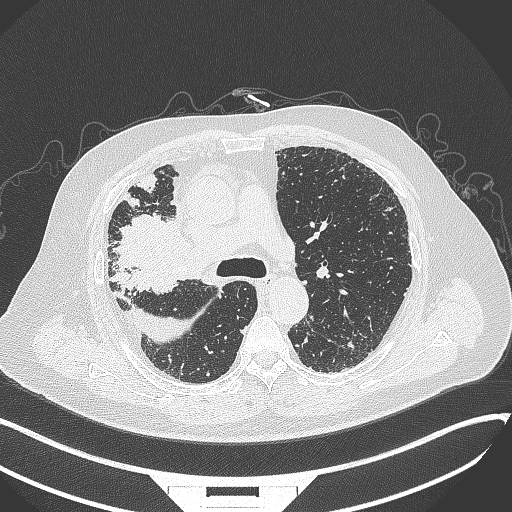
Chest CT, one axial slice. Position 227 of 384 along the scan axis. Reconstruction kernel B70f. Lung window (W 1500 / L -600 HU). 1 mm slice thickness. 512 × 512 image matrix. Male patient, age 69 years. From the clinical record (not read from this slice): clinical TNM (as recorded): T4 N3 M1.
Annotated regions visible in this slice (bounding box drawn by a radiologist):
- lung tumour (recorded histology: adenocarcinoma): bounding box [x1, y1, x2, y2] px = [110, 208, 187, 300]